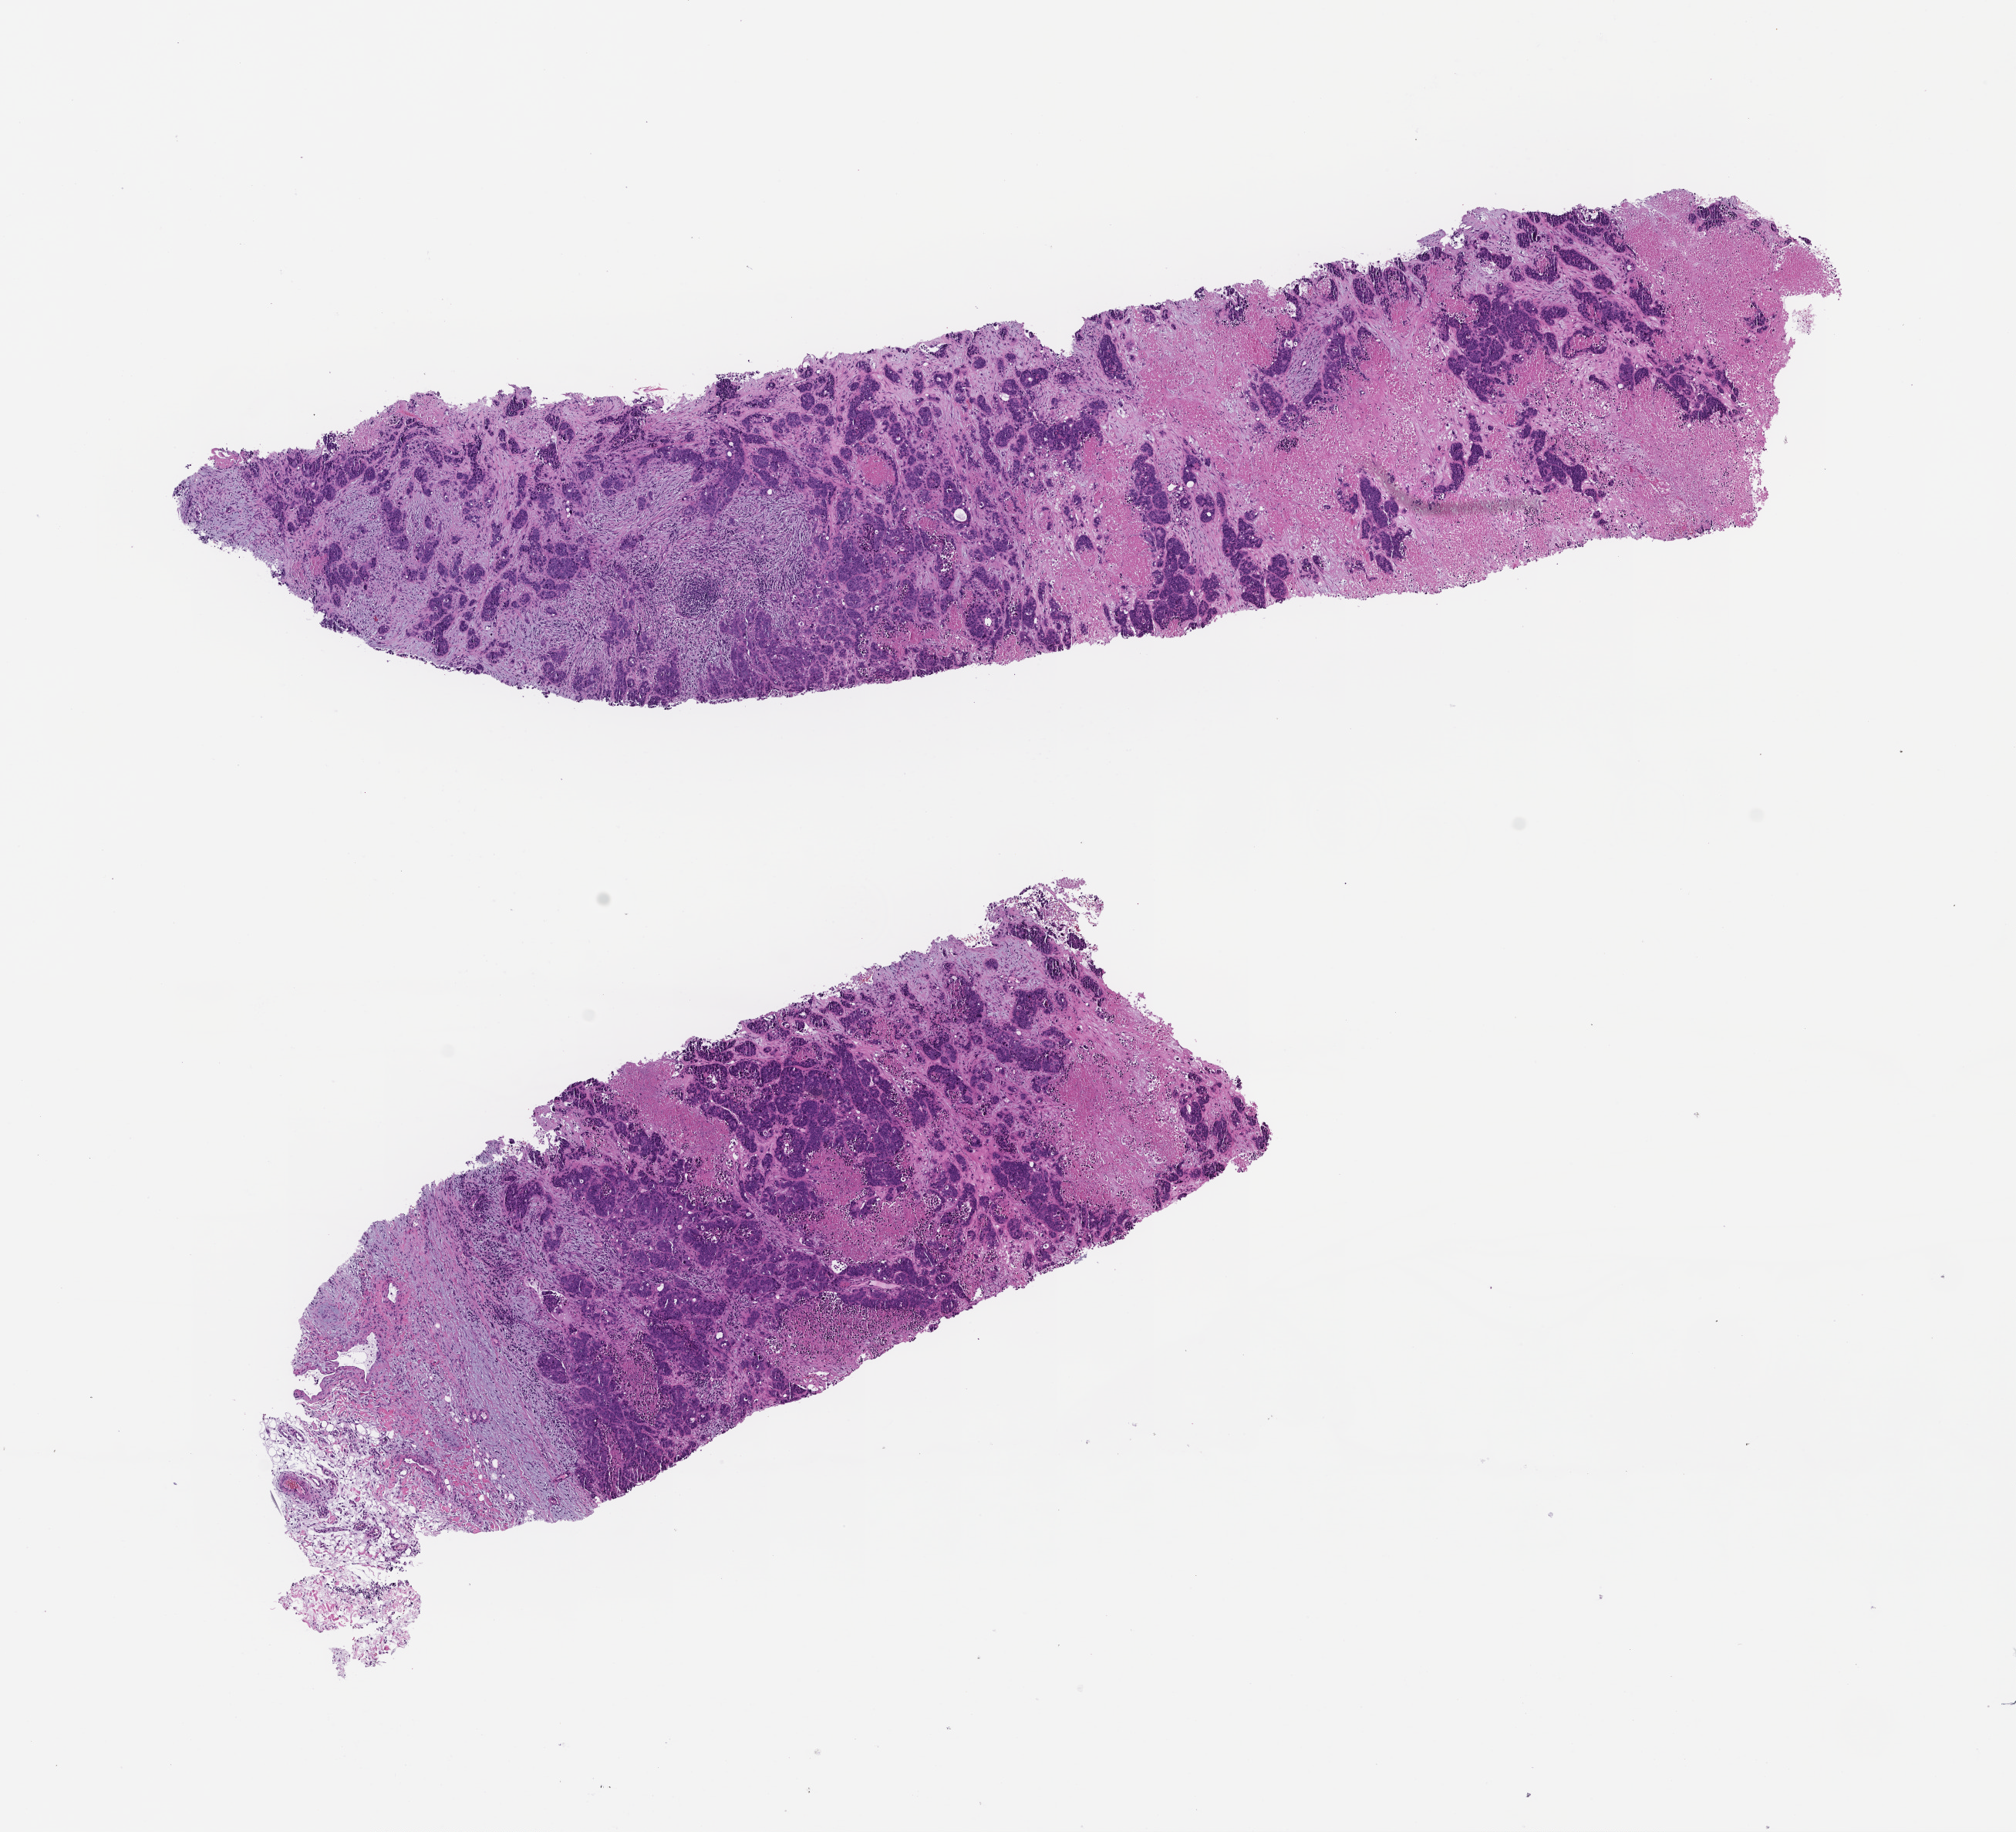
Whole-slide image, H&E stain — whole scanned area (about 10.6 x 9.6 mm) shown as a low-resolution overview; formalin-fixed, paraffin-embedded (FFPE) tissue; site: bone marrow; specimen time point: collected at baseline (before treatment). Patient sex: male.
This section: primary tumor. Diagnosis: Plasma Cell Myeloma.